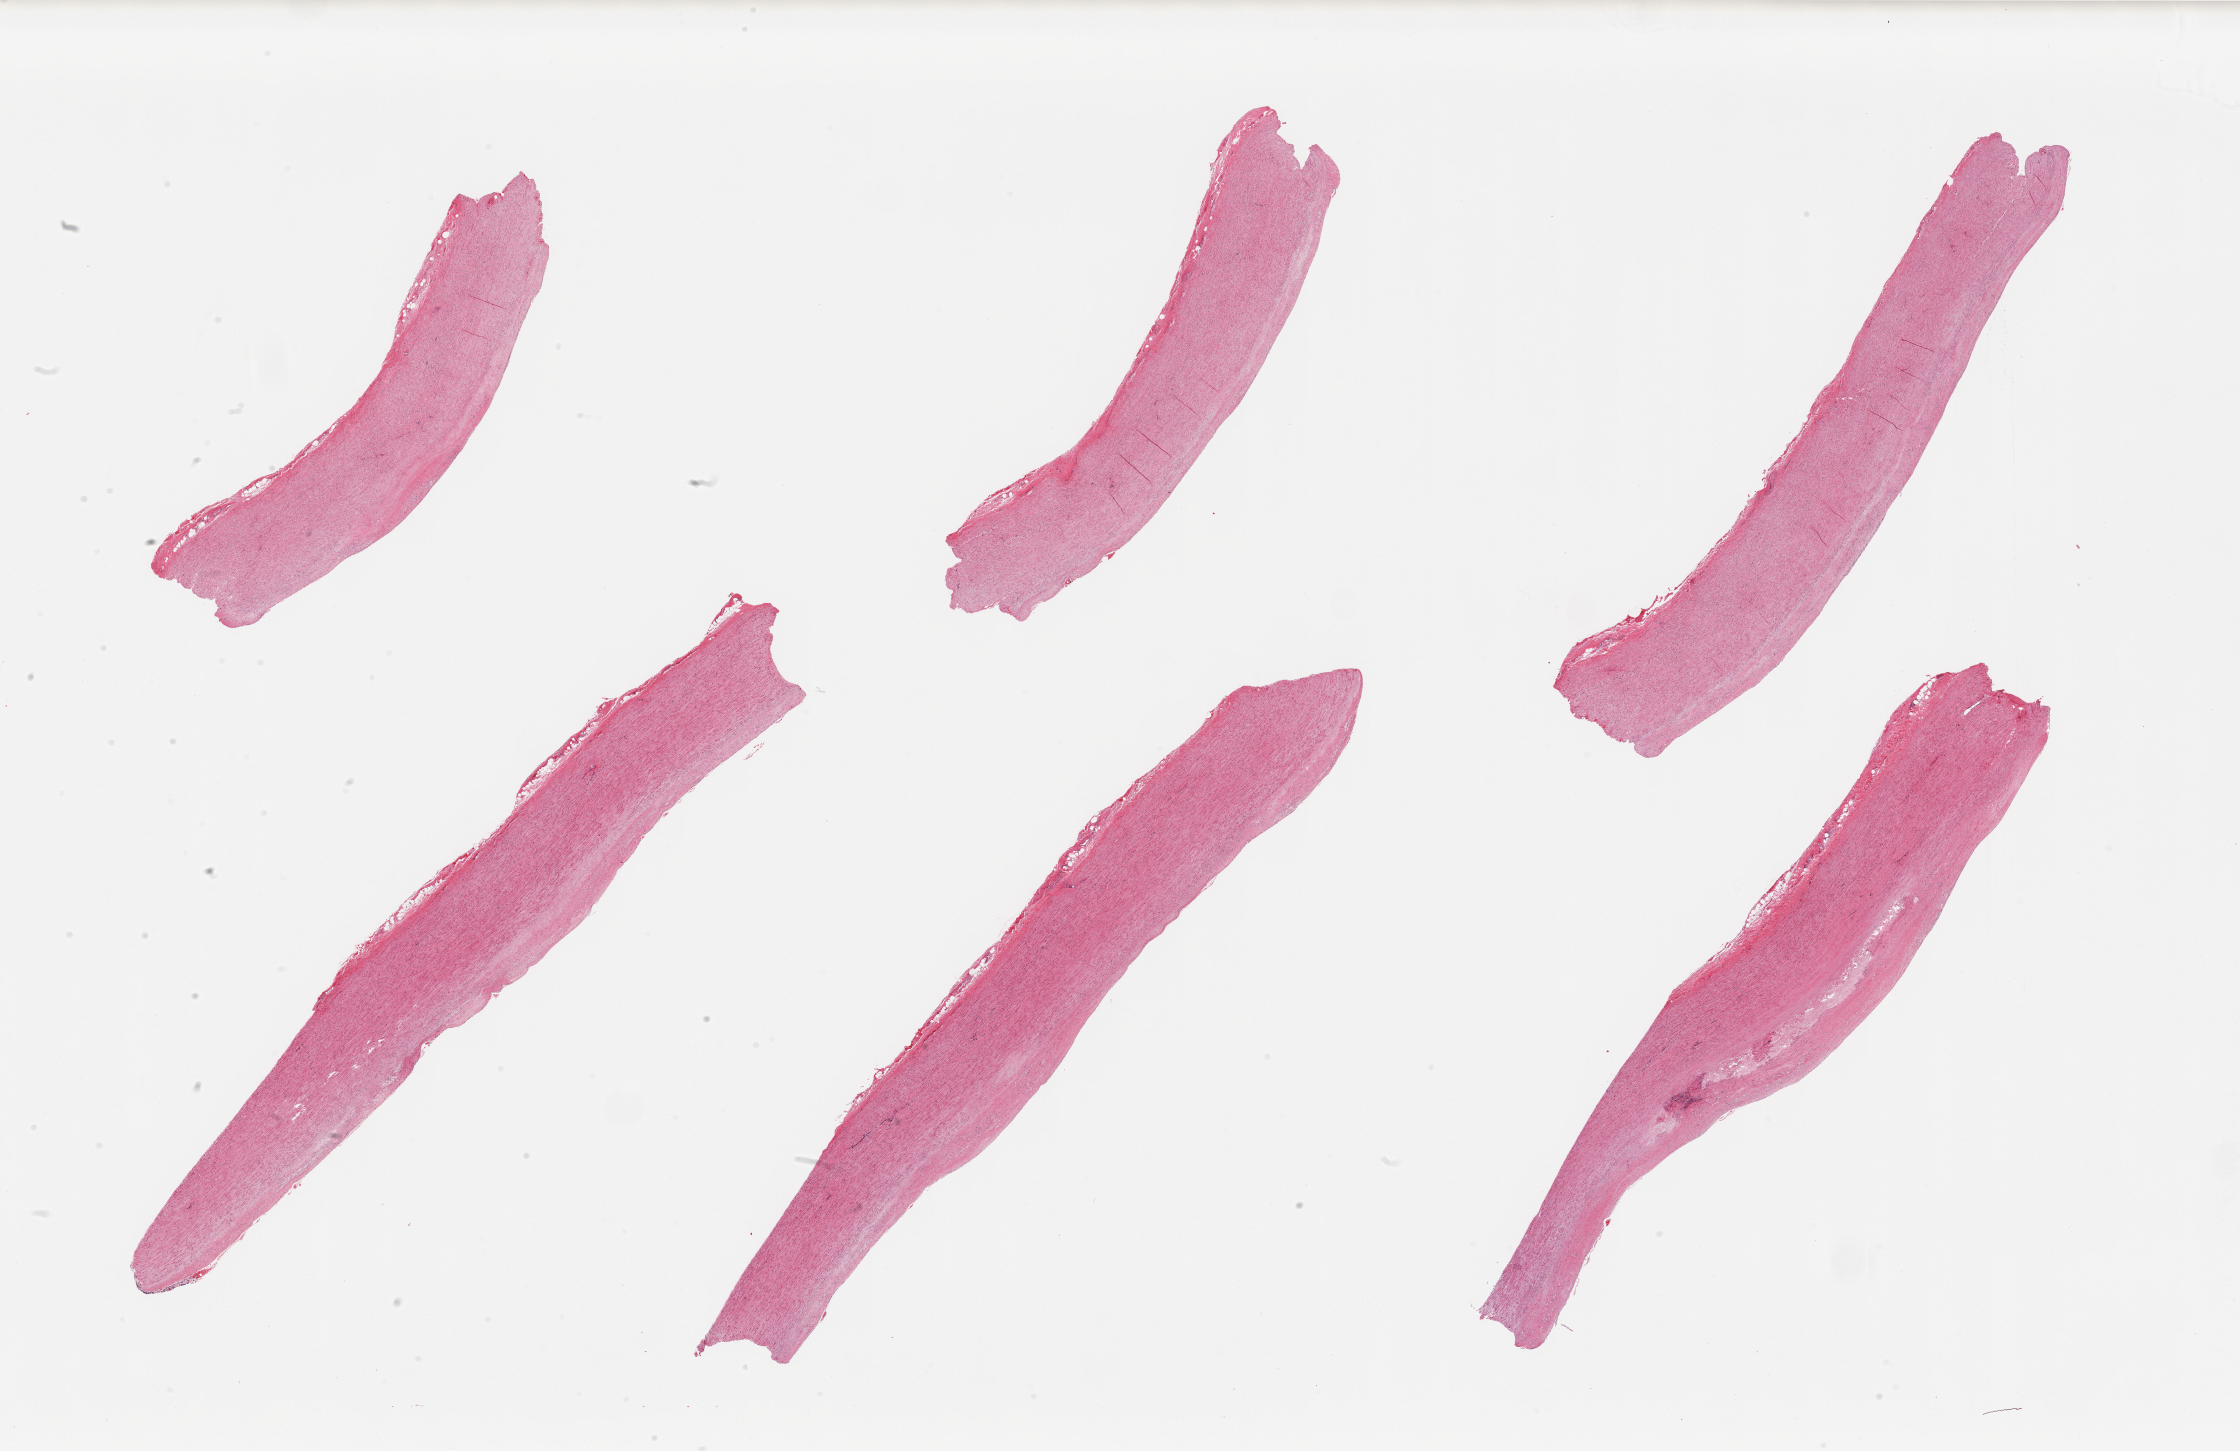
H&E whole-slide image — shown as a low-resolution overview of the whole scanned area (about 35.4 x 23.0 mm); PAXgene-fixed paraffin-embedded (PFPE) section; sampled site (target tissue): aorta; donor tissue sample.
• pathologist's review note for this sample: 6 pieces; atherosclerosis